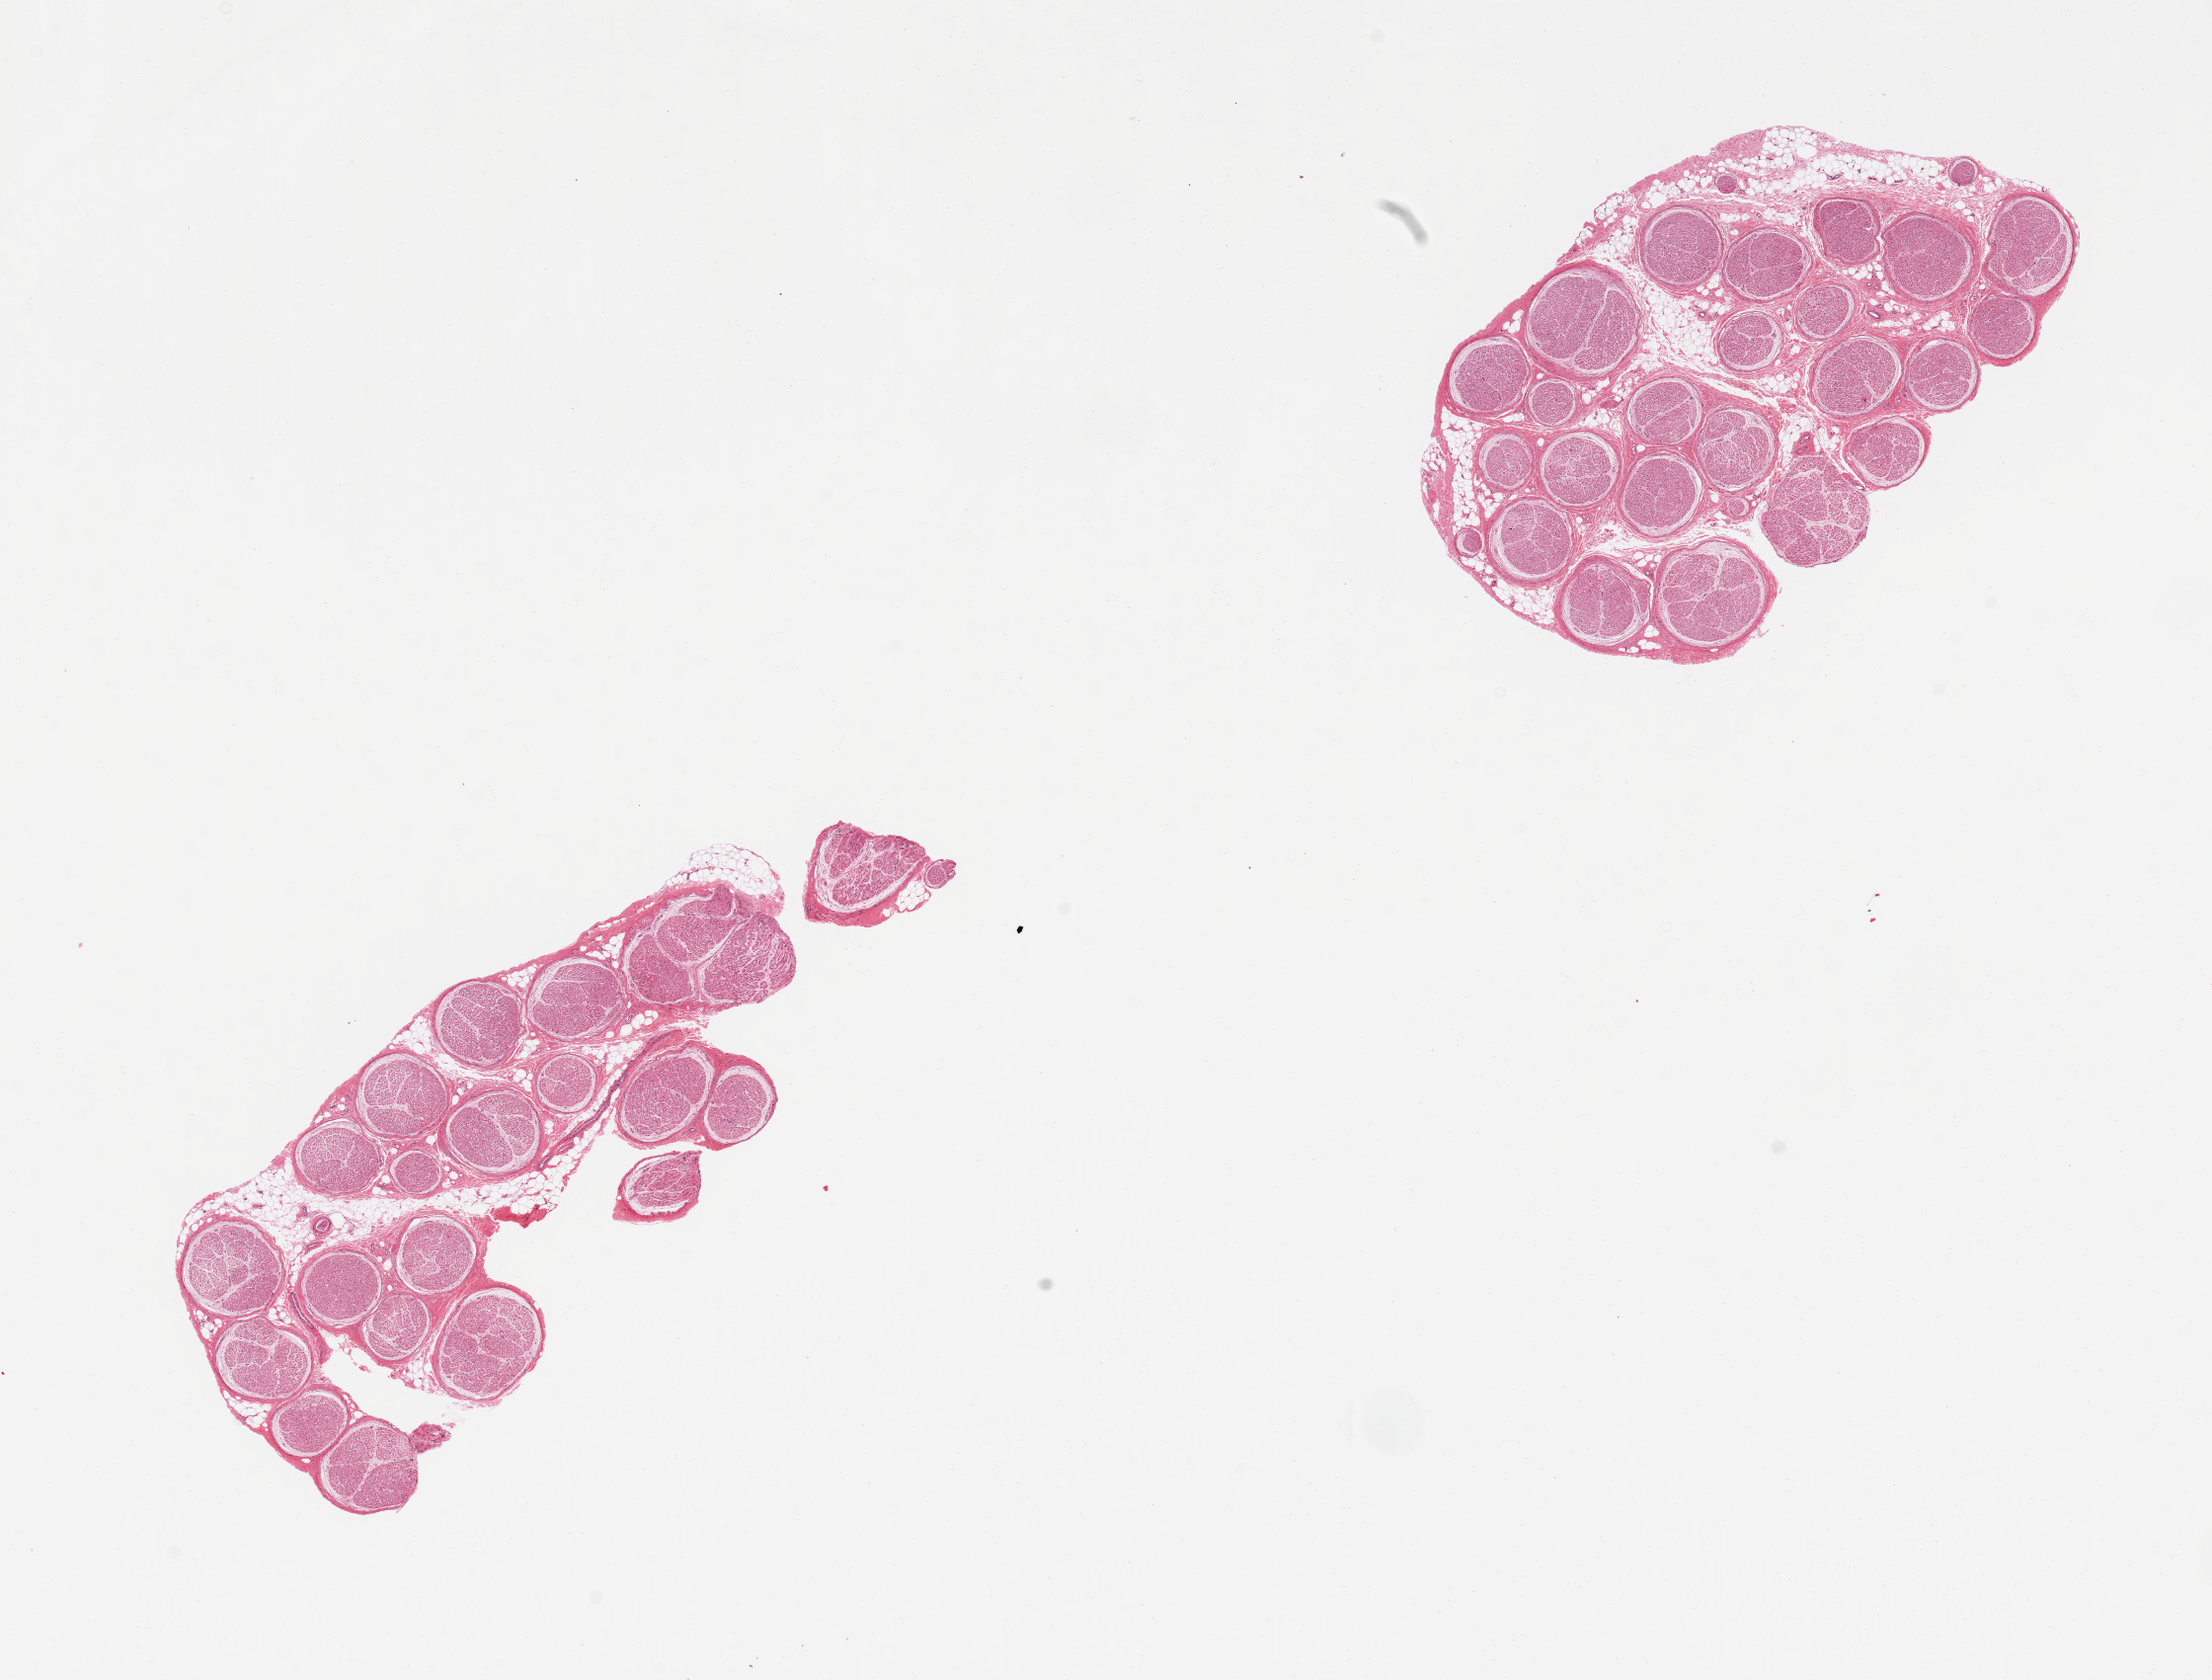
Whole-slide image, haematoxylin and eosin stain — shown as a low-resolution overview of the whole scanned area (about 17.7 x 13.5 mm); PAXgene-fixed, paraffin-embedded tissue; sampled site (target tissue): tibial nerve; tissue donor sample.
- review note (as recorded): 2 pieces; 10% internal fat